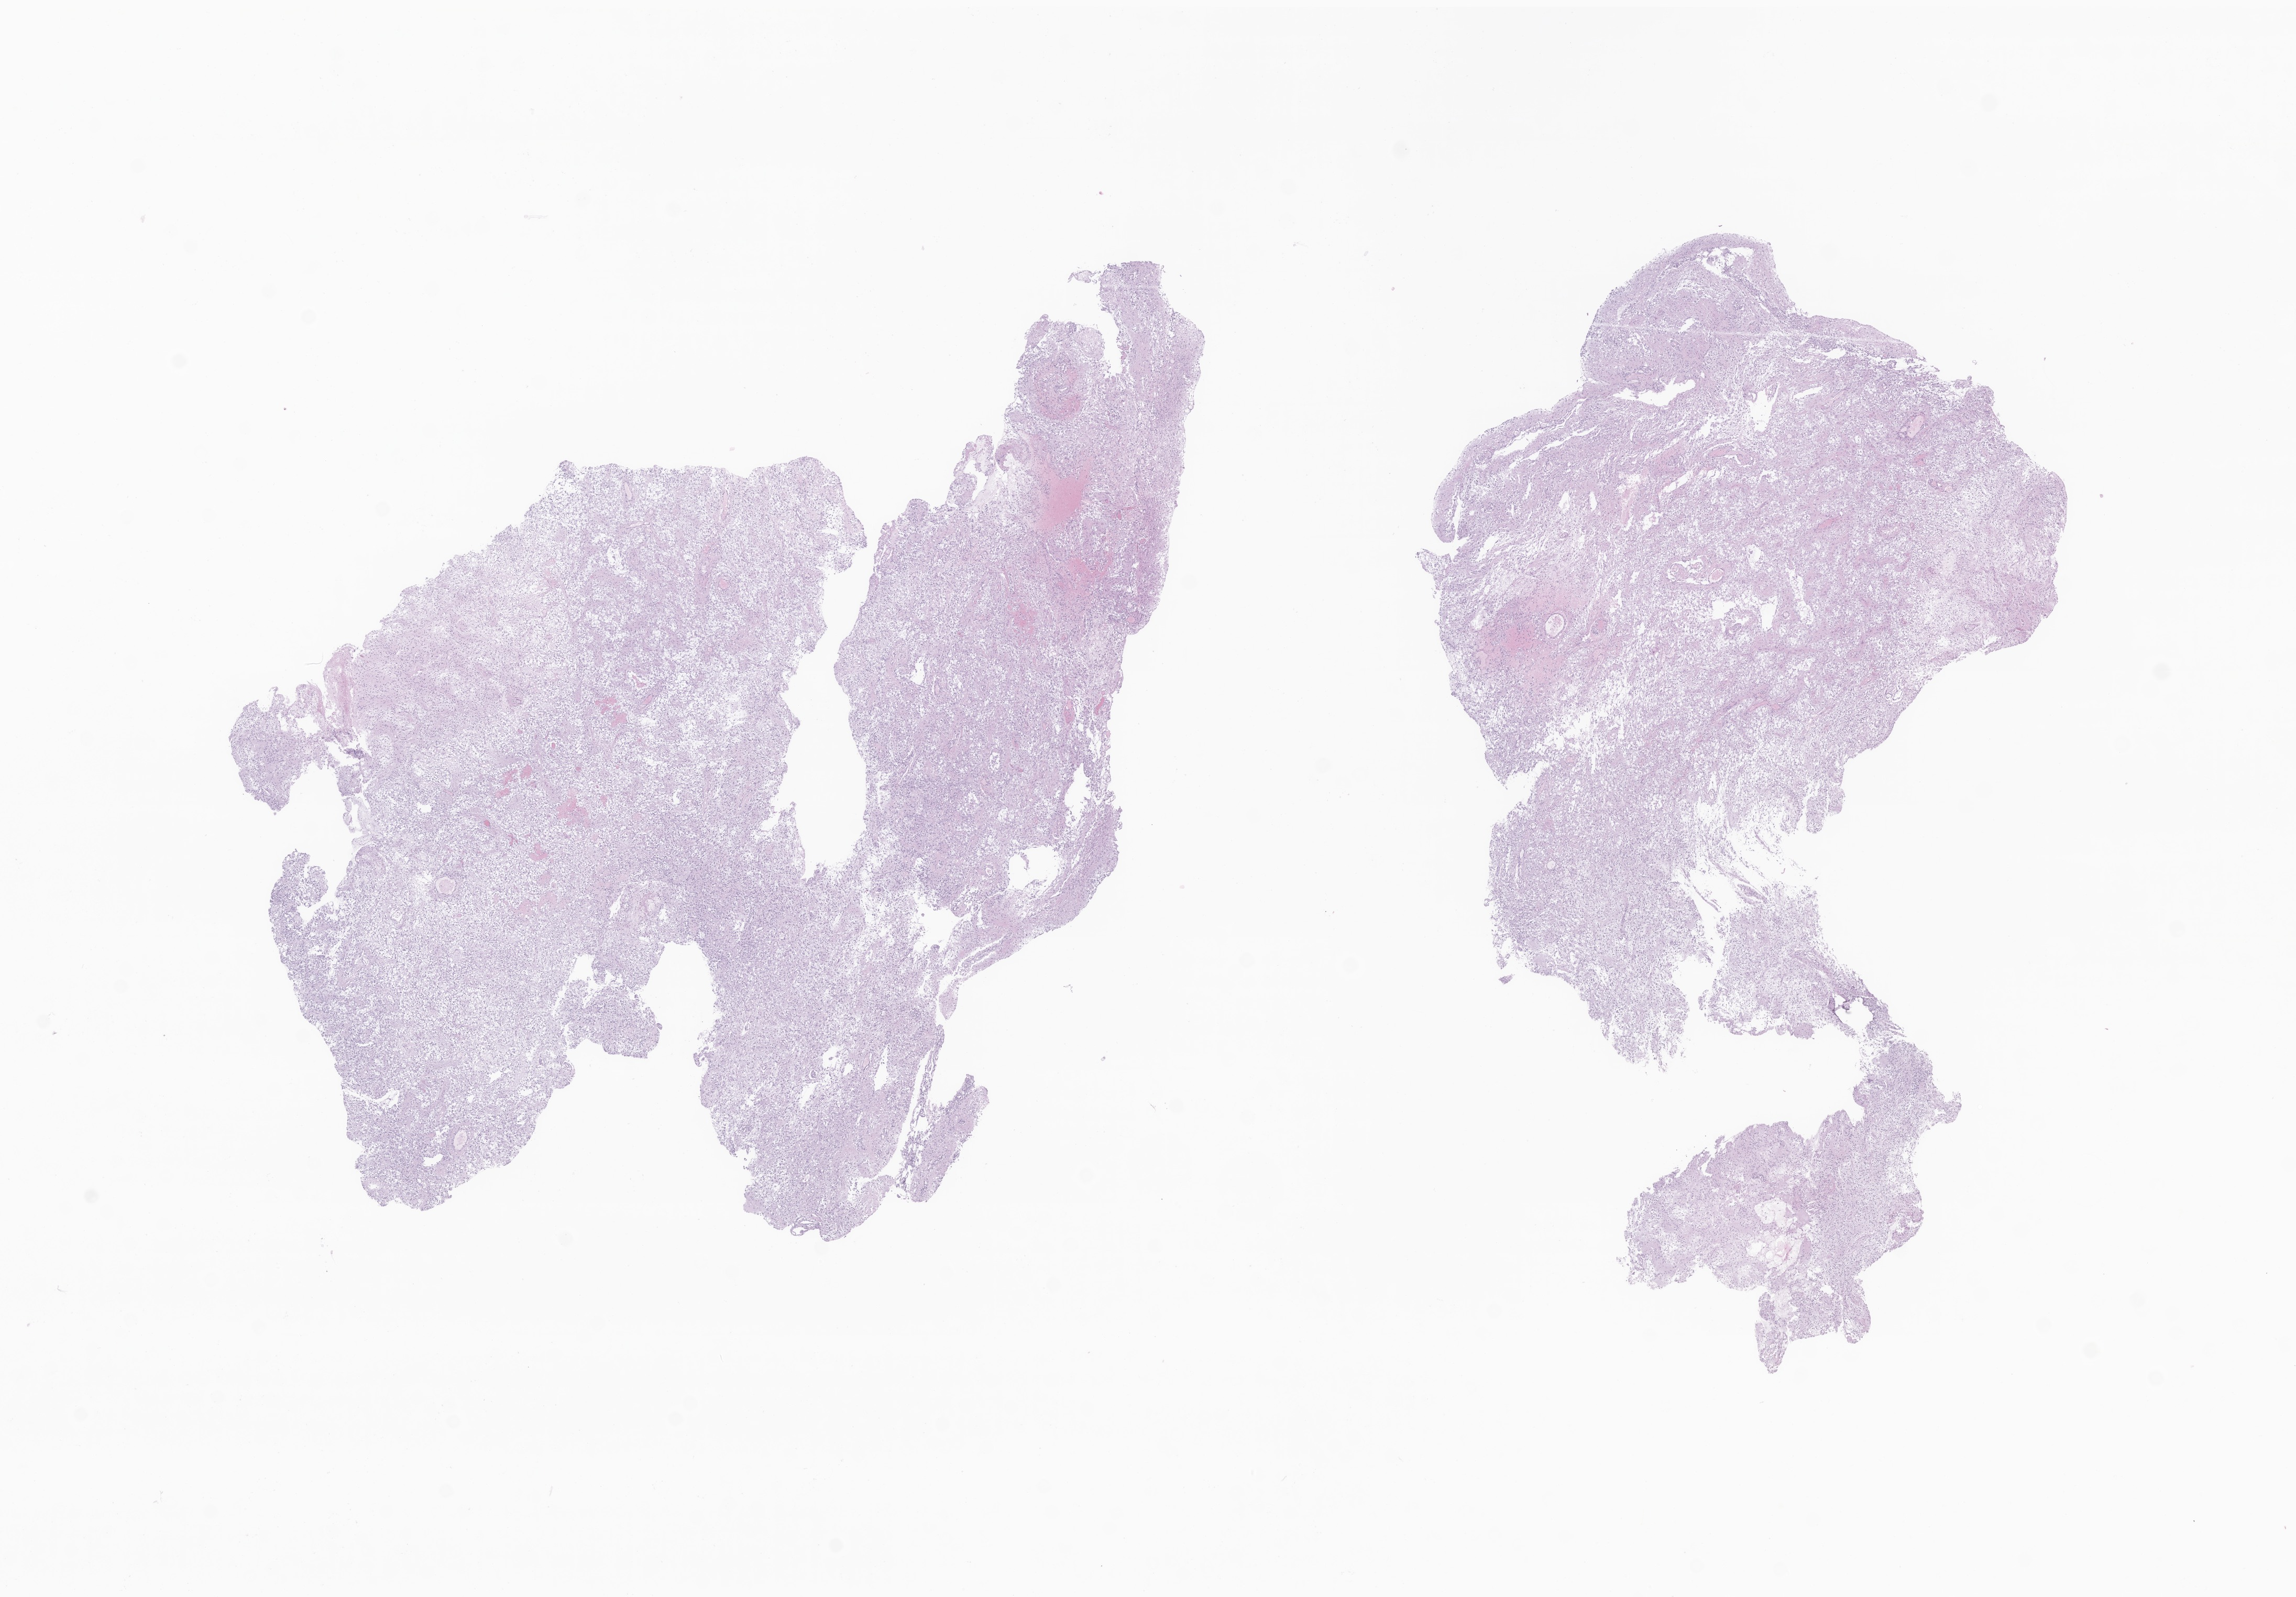
Digitized haematoxylin and eosin-stained section of tumor tissue from the brain, a low-resolution overview of the entire scanned area, about 18.5 x 12.9 mm; formalin-fixed, paraffin-embedded (FFPE) tissue. Patient female; age 100 months (8 years 4 months).
• diagnosis: Pilocytic astrocytoma